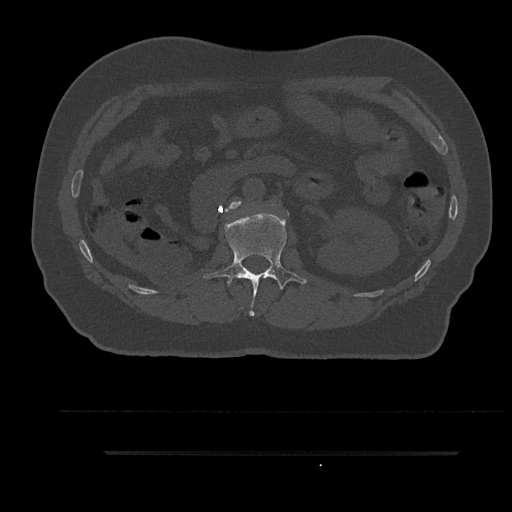
CT including the spine, one axial slice; slice 170 of 797 in the series (ordered by position); 120 kVp; bone window (W 1800 / L 400 HU); 0.5 mm slice thickness; 512 × 512 image matrix. Patient: male, 63 years. From the clinical record (not read from this slice): primary cancer: renal; vertebrae with lytic lesions (as recorded): T8.
Structures marked on this image (semi-automatic segmentation, software-assisted and operator-edited):
- L1 vertebra: bounding box (x1, y1, x2, y2) in pixels: (204, 212, 307, 316)
- L2 vertebra: (225, 201, 241, 211)